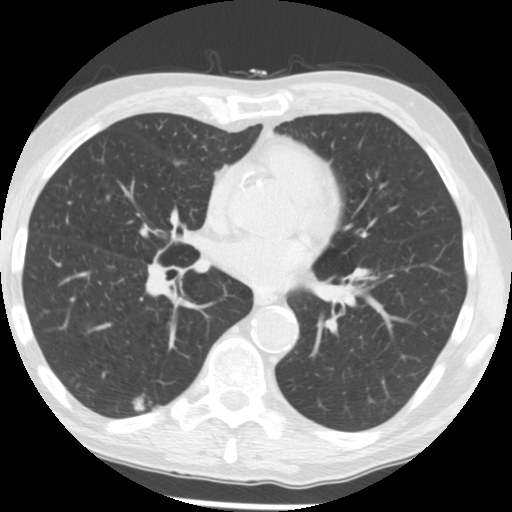
Low-dose screening chest CT, axial slice. Second screening round (one year after baseline). Lung window (W 1500 / L -600 HU). 512 × 512 image matrix, field of view 327 × 327 mm. Male, age 62 years at enrolment. Current smoker at enrolment.
- Expert reader's lesion annotation, bounding box <122,389,159,426> (left, top, right, bottom; pixels).
- The screening reader recorded 2 non-calcified nodules or masses ≥4 mm on this exam; which of them this box marks is not recorded.
- Official screen result: positive, change unspecified: nodule(s) >= 4 mm or enlarging nodule(s), mass(es), or other non-specific abnormalities suspicious for lung cancer.
- Later outcome: lung cancer diagnosed 506 days after this screen — adenocarcinoma, NOS, right lower lobe, moderately differentiated (G2), stage IIIB (AJCC 6th edition), 15 mm at pathology.